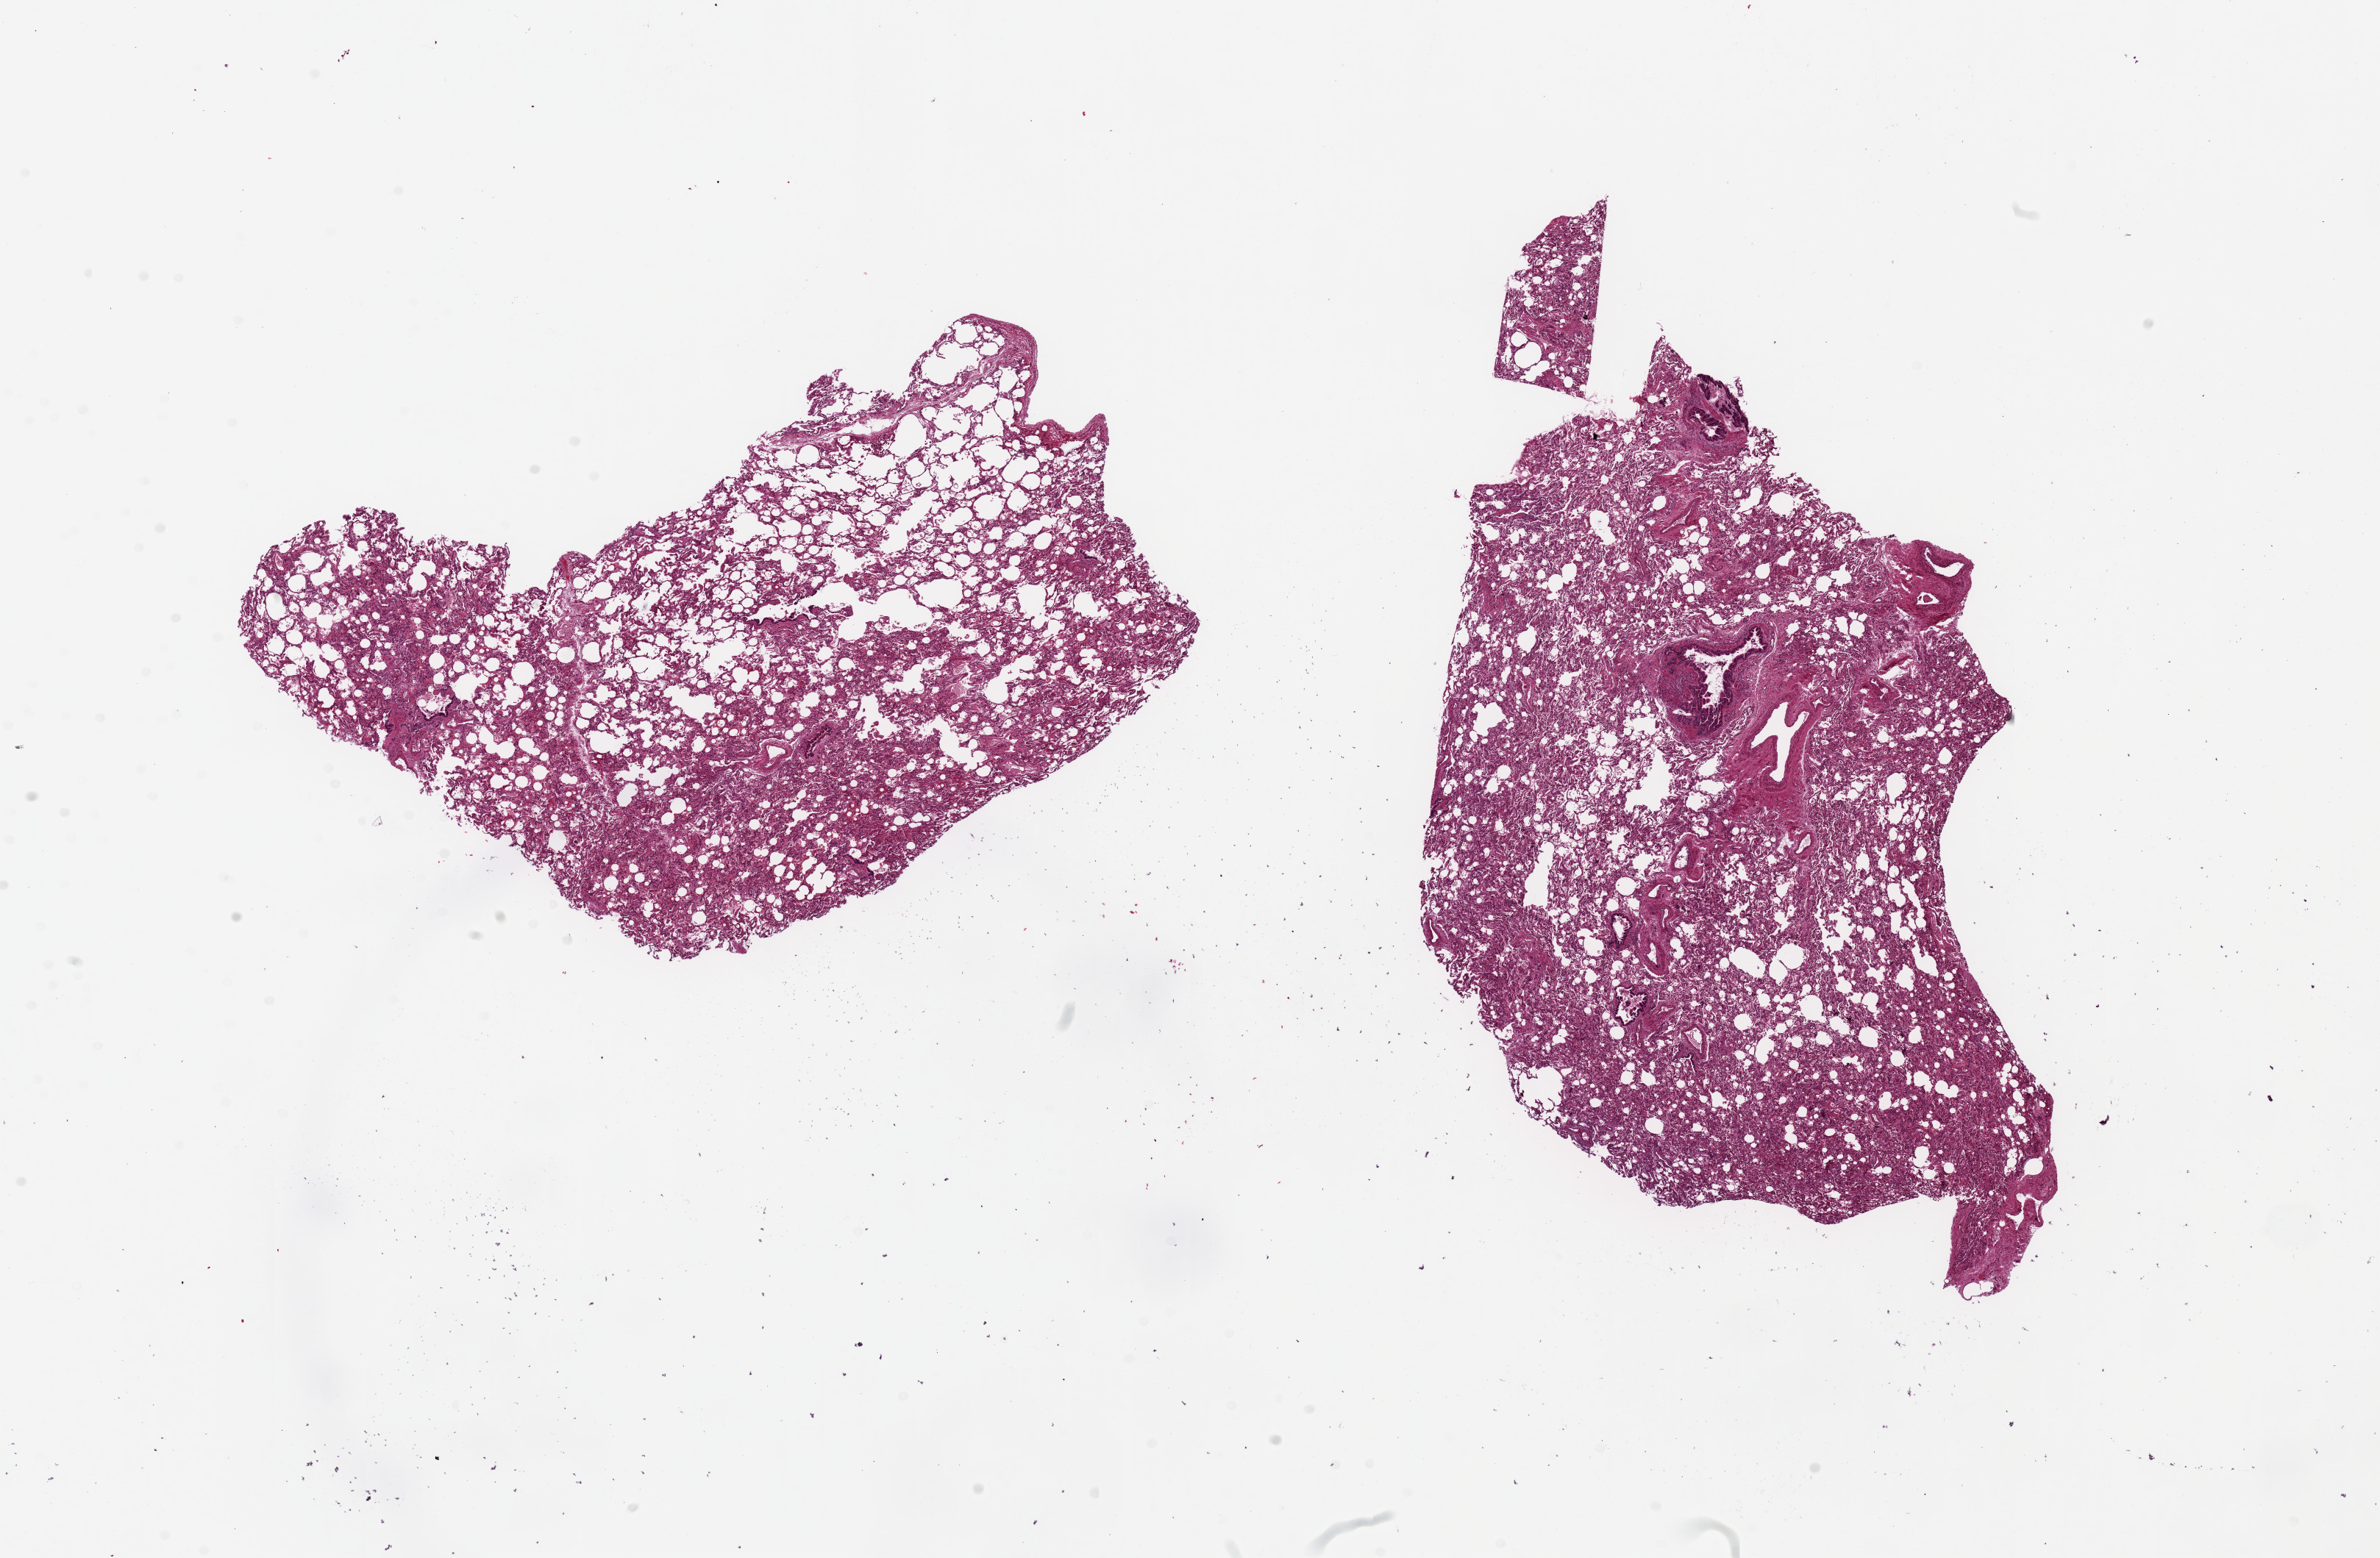
Hematoxylin and eosin (H&E) whole-slide image — shown as a low-resolution overview of the whole scanned area (about 25.6 x 16.8 mm); PAXgene-fixed, paraffin-embedded tissue; sampled site (target tissue): lung; donor tissue sample. Donor: male.
Review note (as recorded): 2 pieces ~7x6mm Unusally well preserved, well visualized and preserved bronchial structures noted.